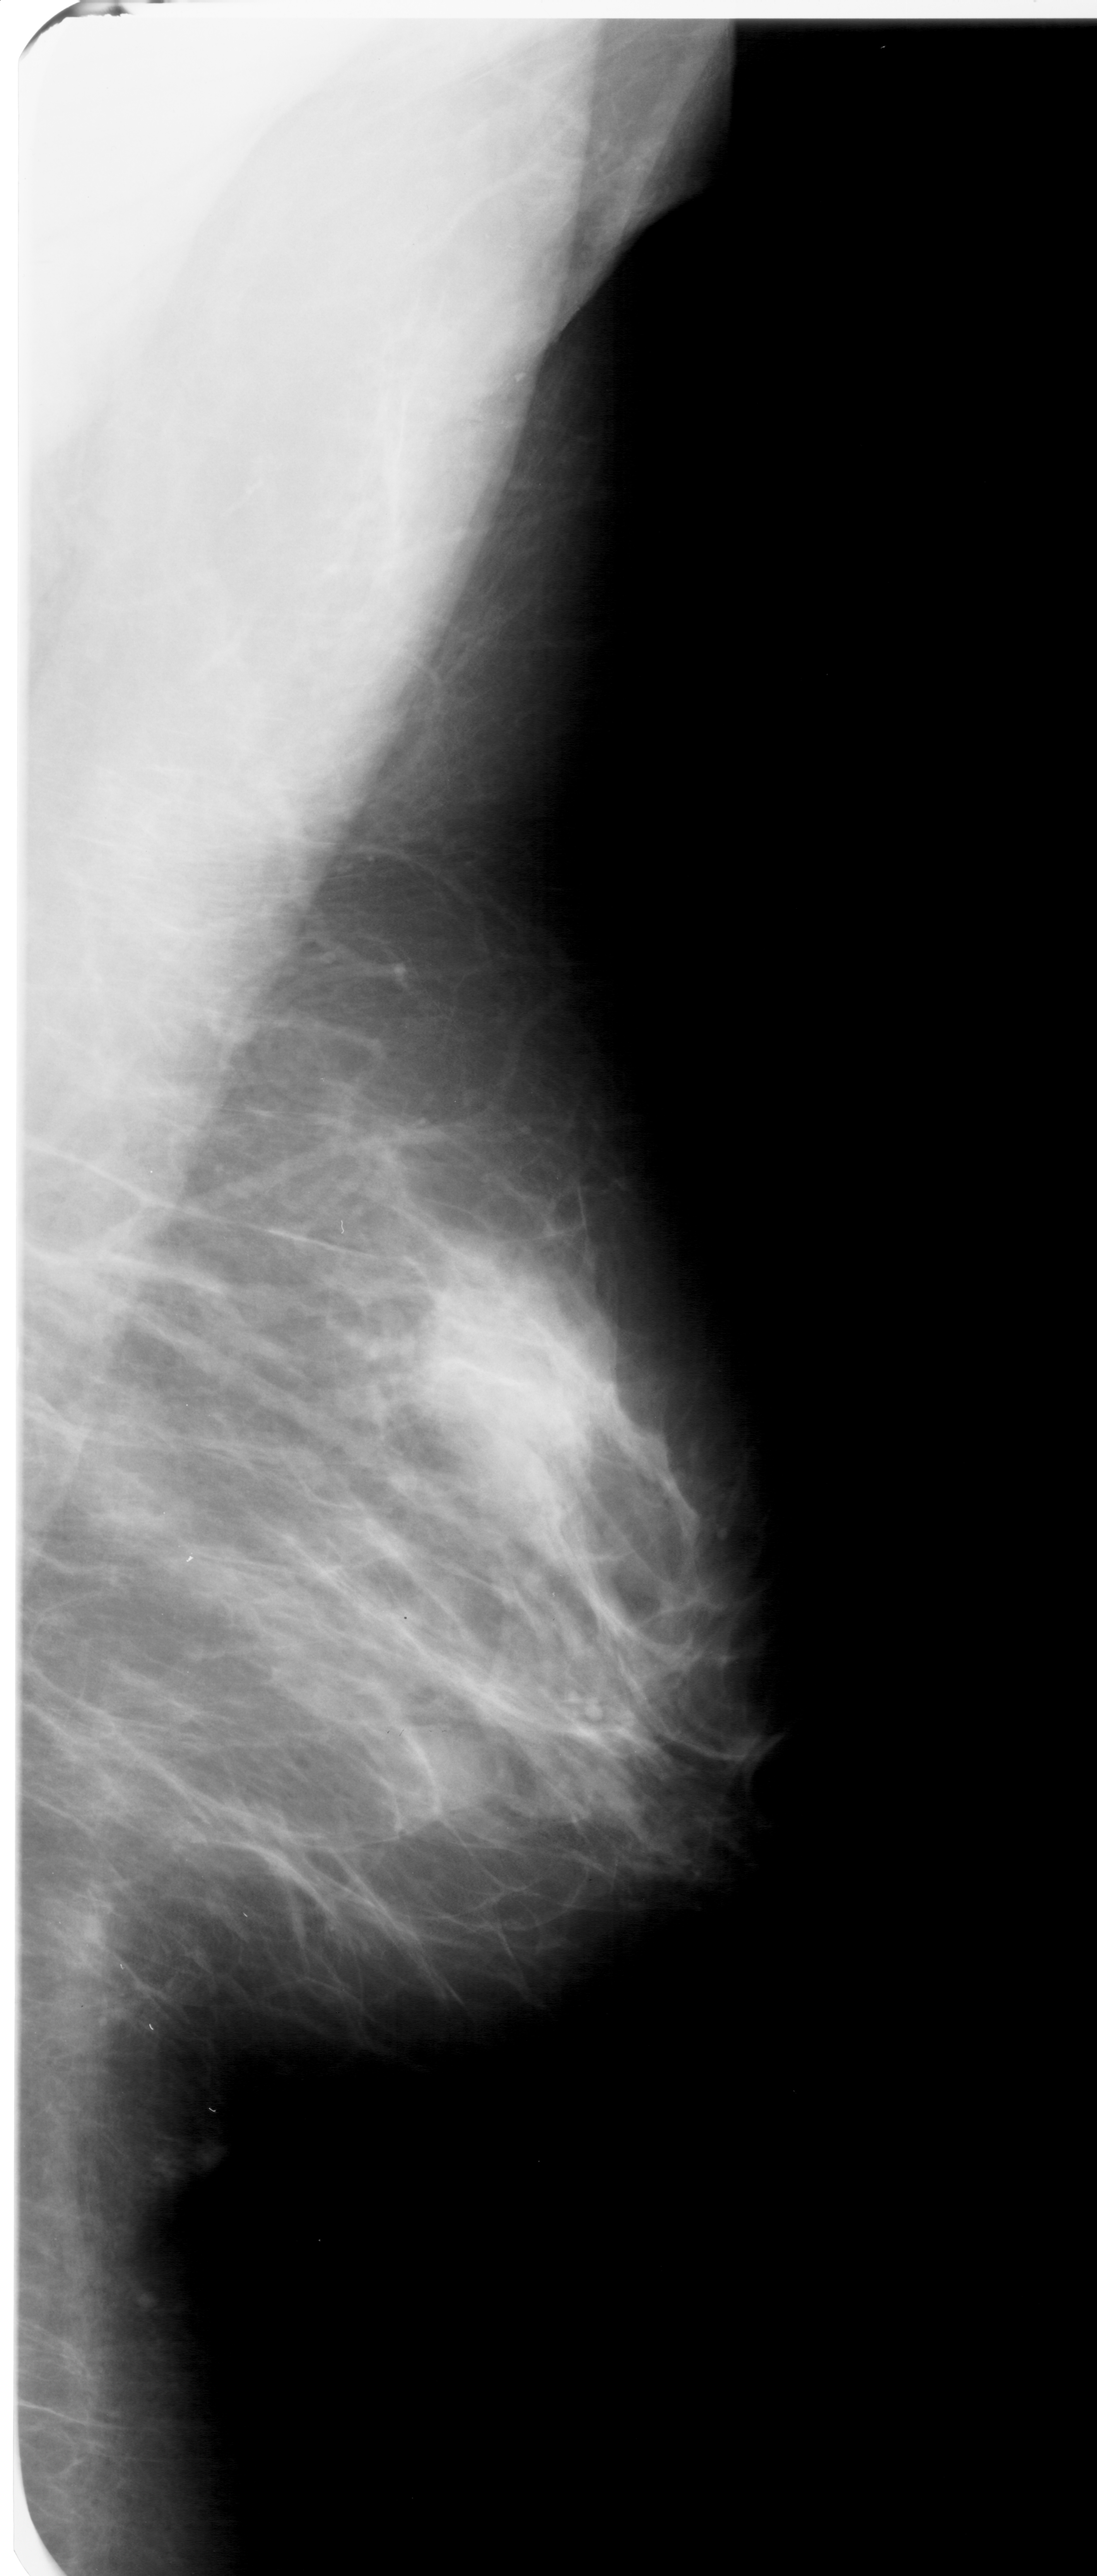
Scanned film-screen mammogram; right breast; mediolateral oblique (MLO) view; BI-RADS breast density category 1 (scale 1–4); 1097 × 2576 image matrix.
Expert-marked regions of interest on this image (one box per marked abnormality):
- mass, shape oval, margins obscured; BI-RADS assessment category 3; pathology result (as recorded, not read from the image): benign: bounding box (x1, y1, x2, y2) in pixels: (385, 1705, 508, 1838)